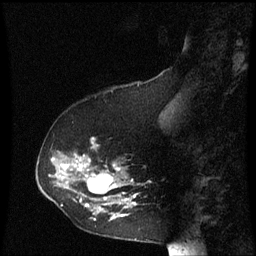
Breast MRI (dynamic contrast-enhanced), one sagittal slice. Slice 21 of 60 in the series (ordered by position). Dynamic contrast-enhanced series, image 2 of 3 at this slice position (ordered by acquisition). 1.5 T. TE 4.2 ms, TR 8.9 ms. 2 mm slice thickness. 256 × 256 image matrix, field of view 200 × 200 mm. Female patient, age 53 years. Case-level facts recorded for this patient, not image findings: setting: breast cancer imaged before/during neoadjuvant chemotherapy; receptor status: HR-positive, HER2-negative.
Annotated regions visible in this slice (semi-automatic segmentation, software-assisted and operator-edited):
- analysis volume of interest (the breast-tissue region the enhancement analysis was run in; not a lesion): box from (x=38, y=138) to (x=141, y=221) px
- tumour enhancement mask (voxels above the 70 % enhancement threshold inside the analysis volume of interest): (x=52, y=140)–(x=137, y=219)